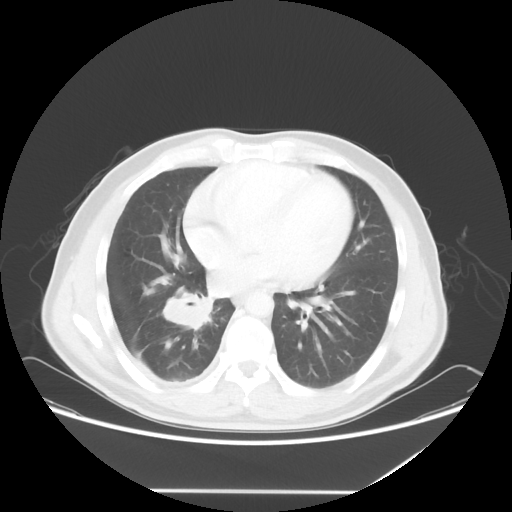
Chest CT, one axial slice; position 26 of 60 along the scan axis; reconstruction kernel STANDARD; lung window (W 1500 / L -600 HU); 5 mm slice thickness; 512 × 512 image matrix, field of view 419 × 419 mm. Male patient, age 48 years. Case-level facts recorded for this patient, not image findings: clinical TNM (as recorded): T3 N3 M1a.
Annotated regions visible in this slice (rectangle marked by the reading radiologist):
- lung tumour (recorded histology: squamous cell carcinoma): bounding box <161,286,219,332> (left, top, right, bottom; pixels)